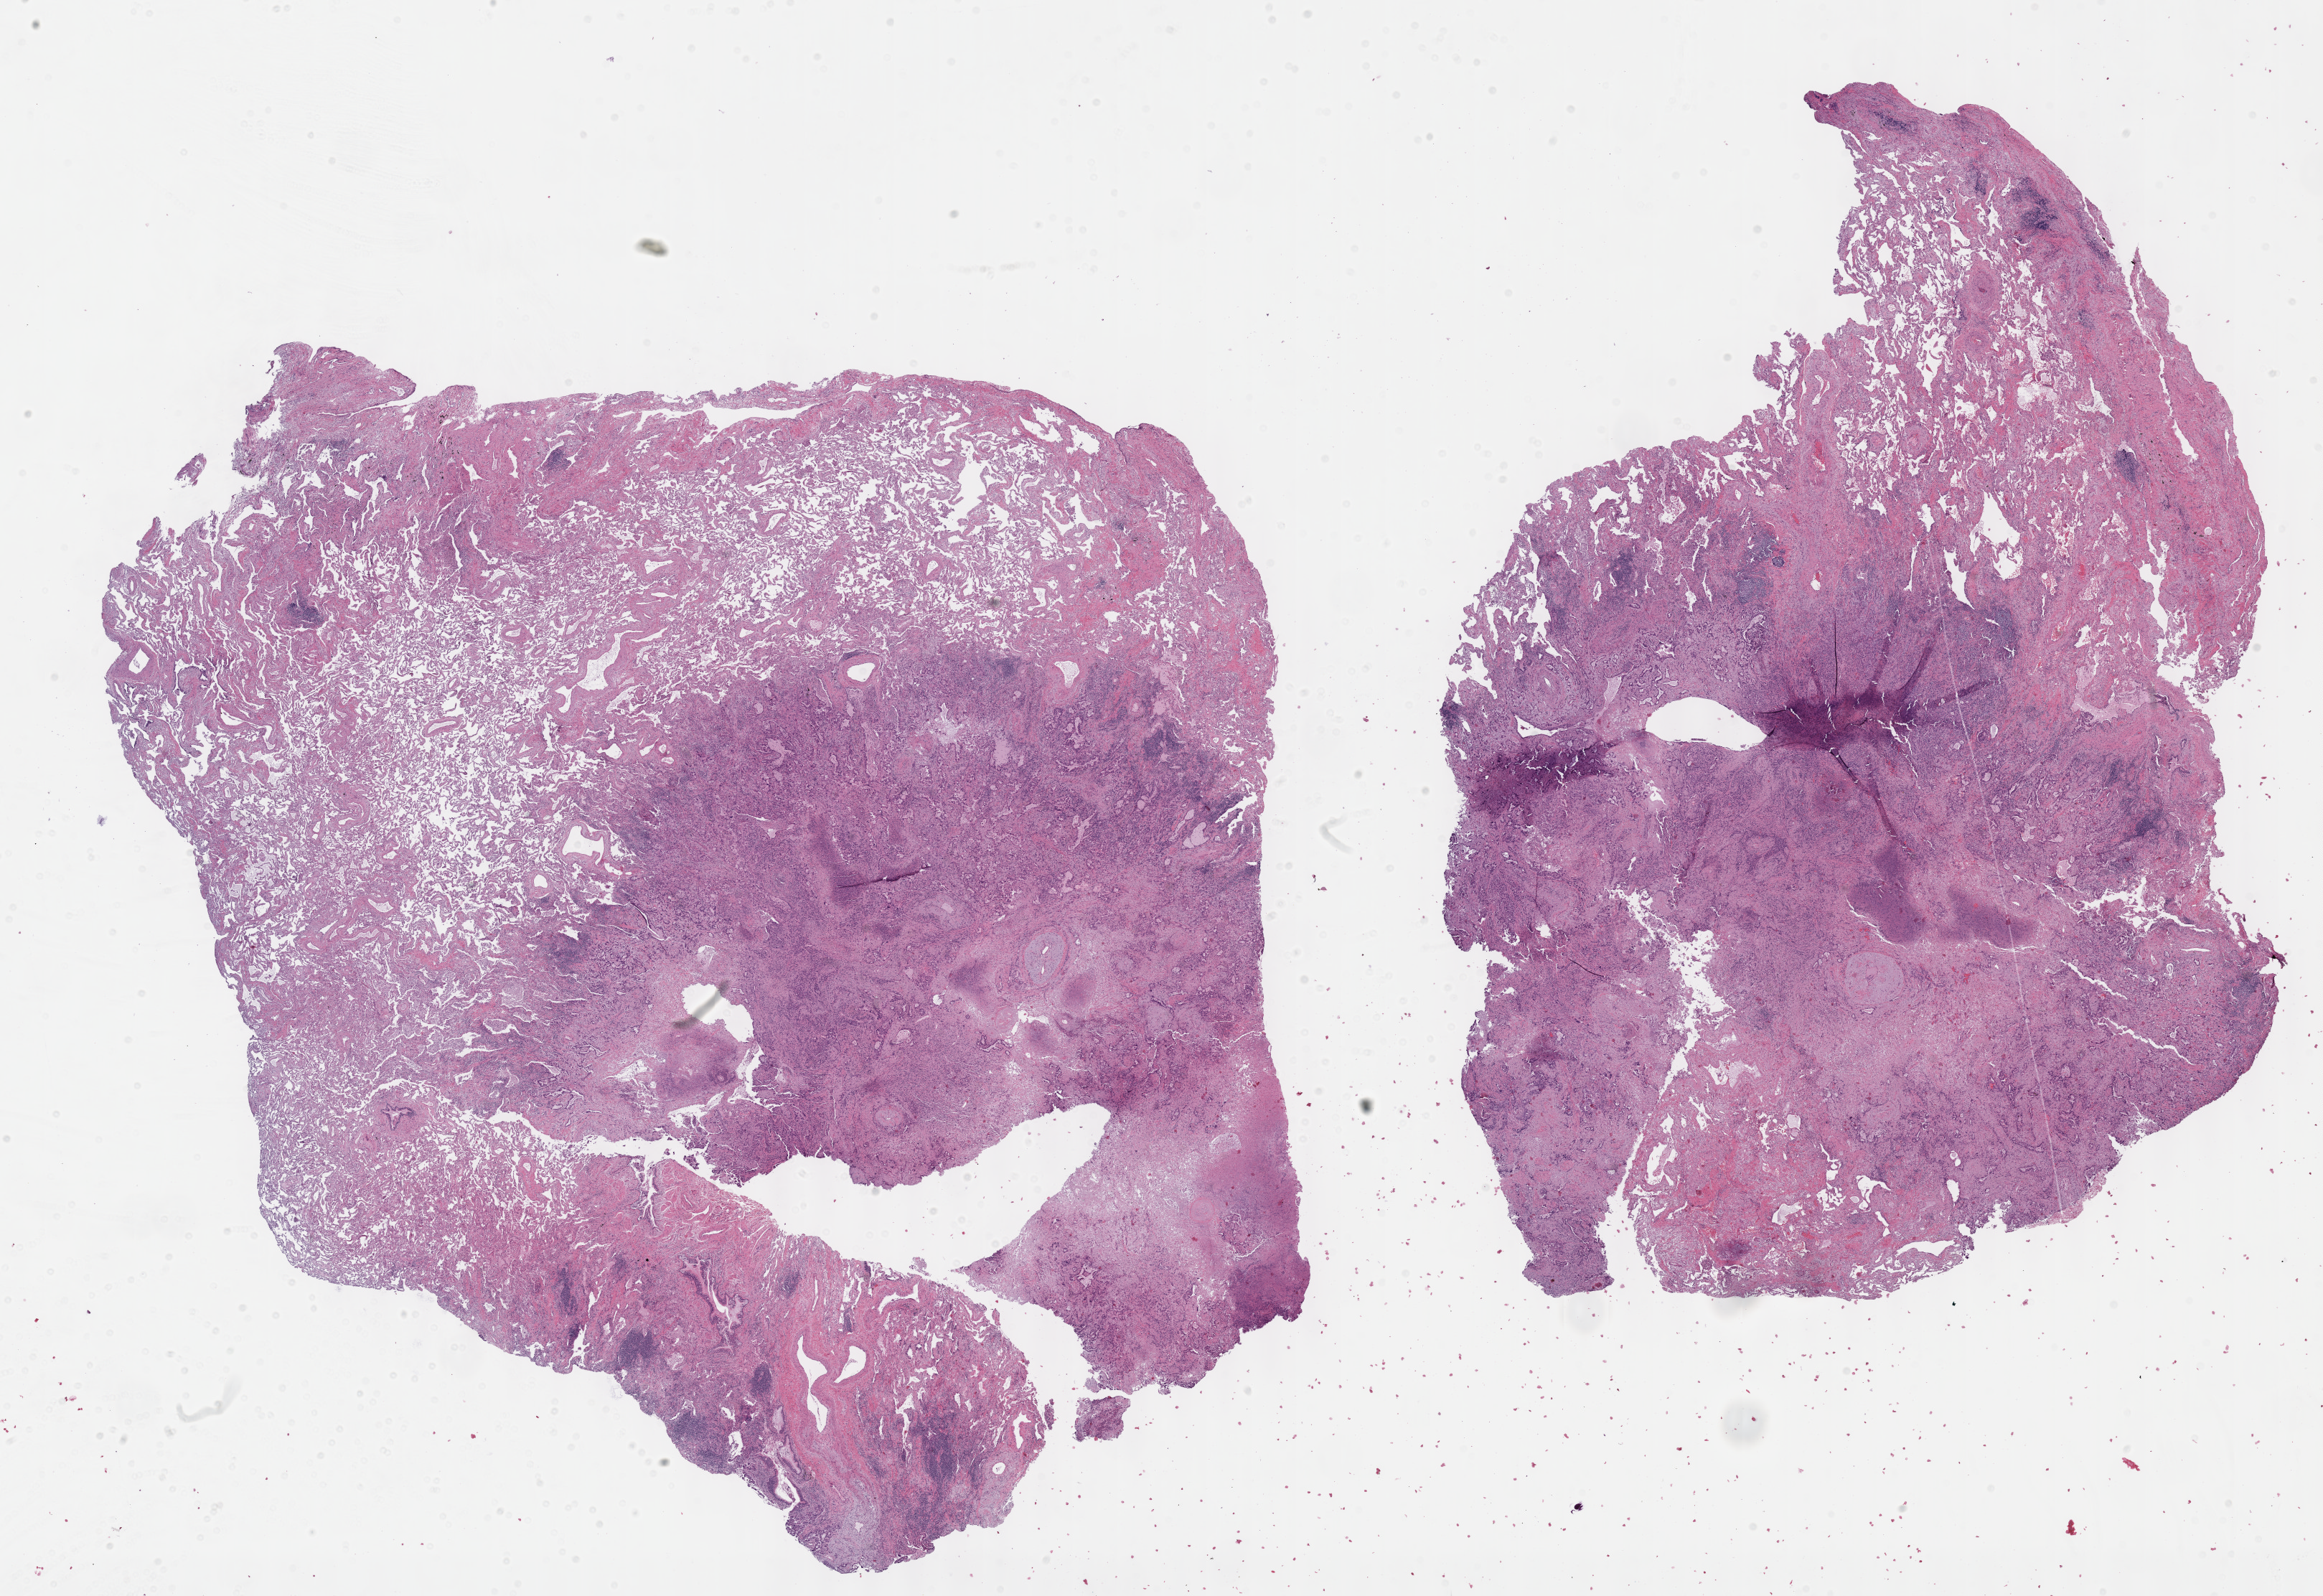
Digitized Hematoxylin and eosin (H&E) stained tissue section (whole slide), a low-resolution overview of the entire scanned area, about 26.2 x 18.0 mm (acquisition: 40x scan). FFPE section. Lung, primary tumour sample. Male patient; age at initial diagnosis 77 years.
AJCC pathologic stage: IIIA. Laterality: right. Histologic diagnosis: Adenocarcinoma, NOS.